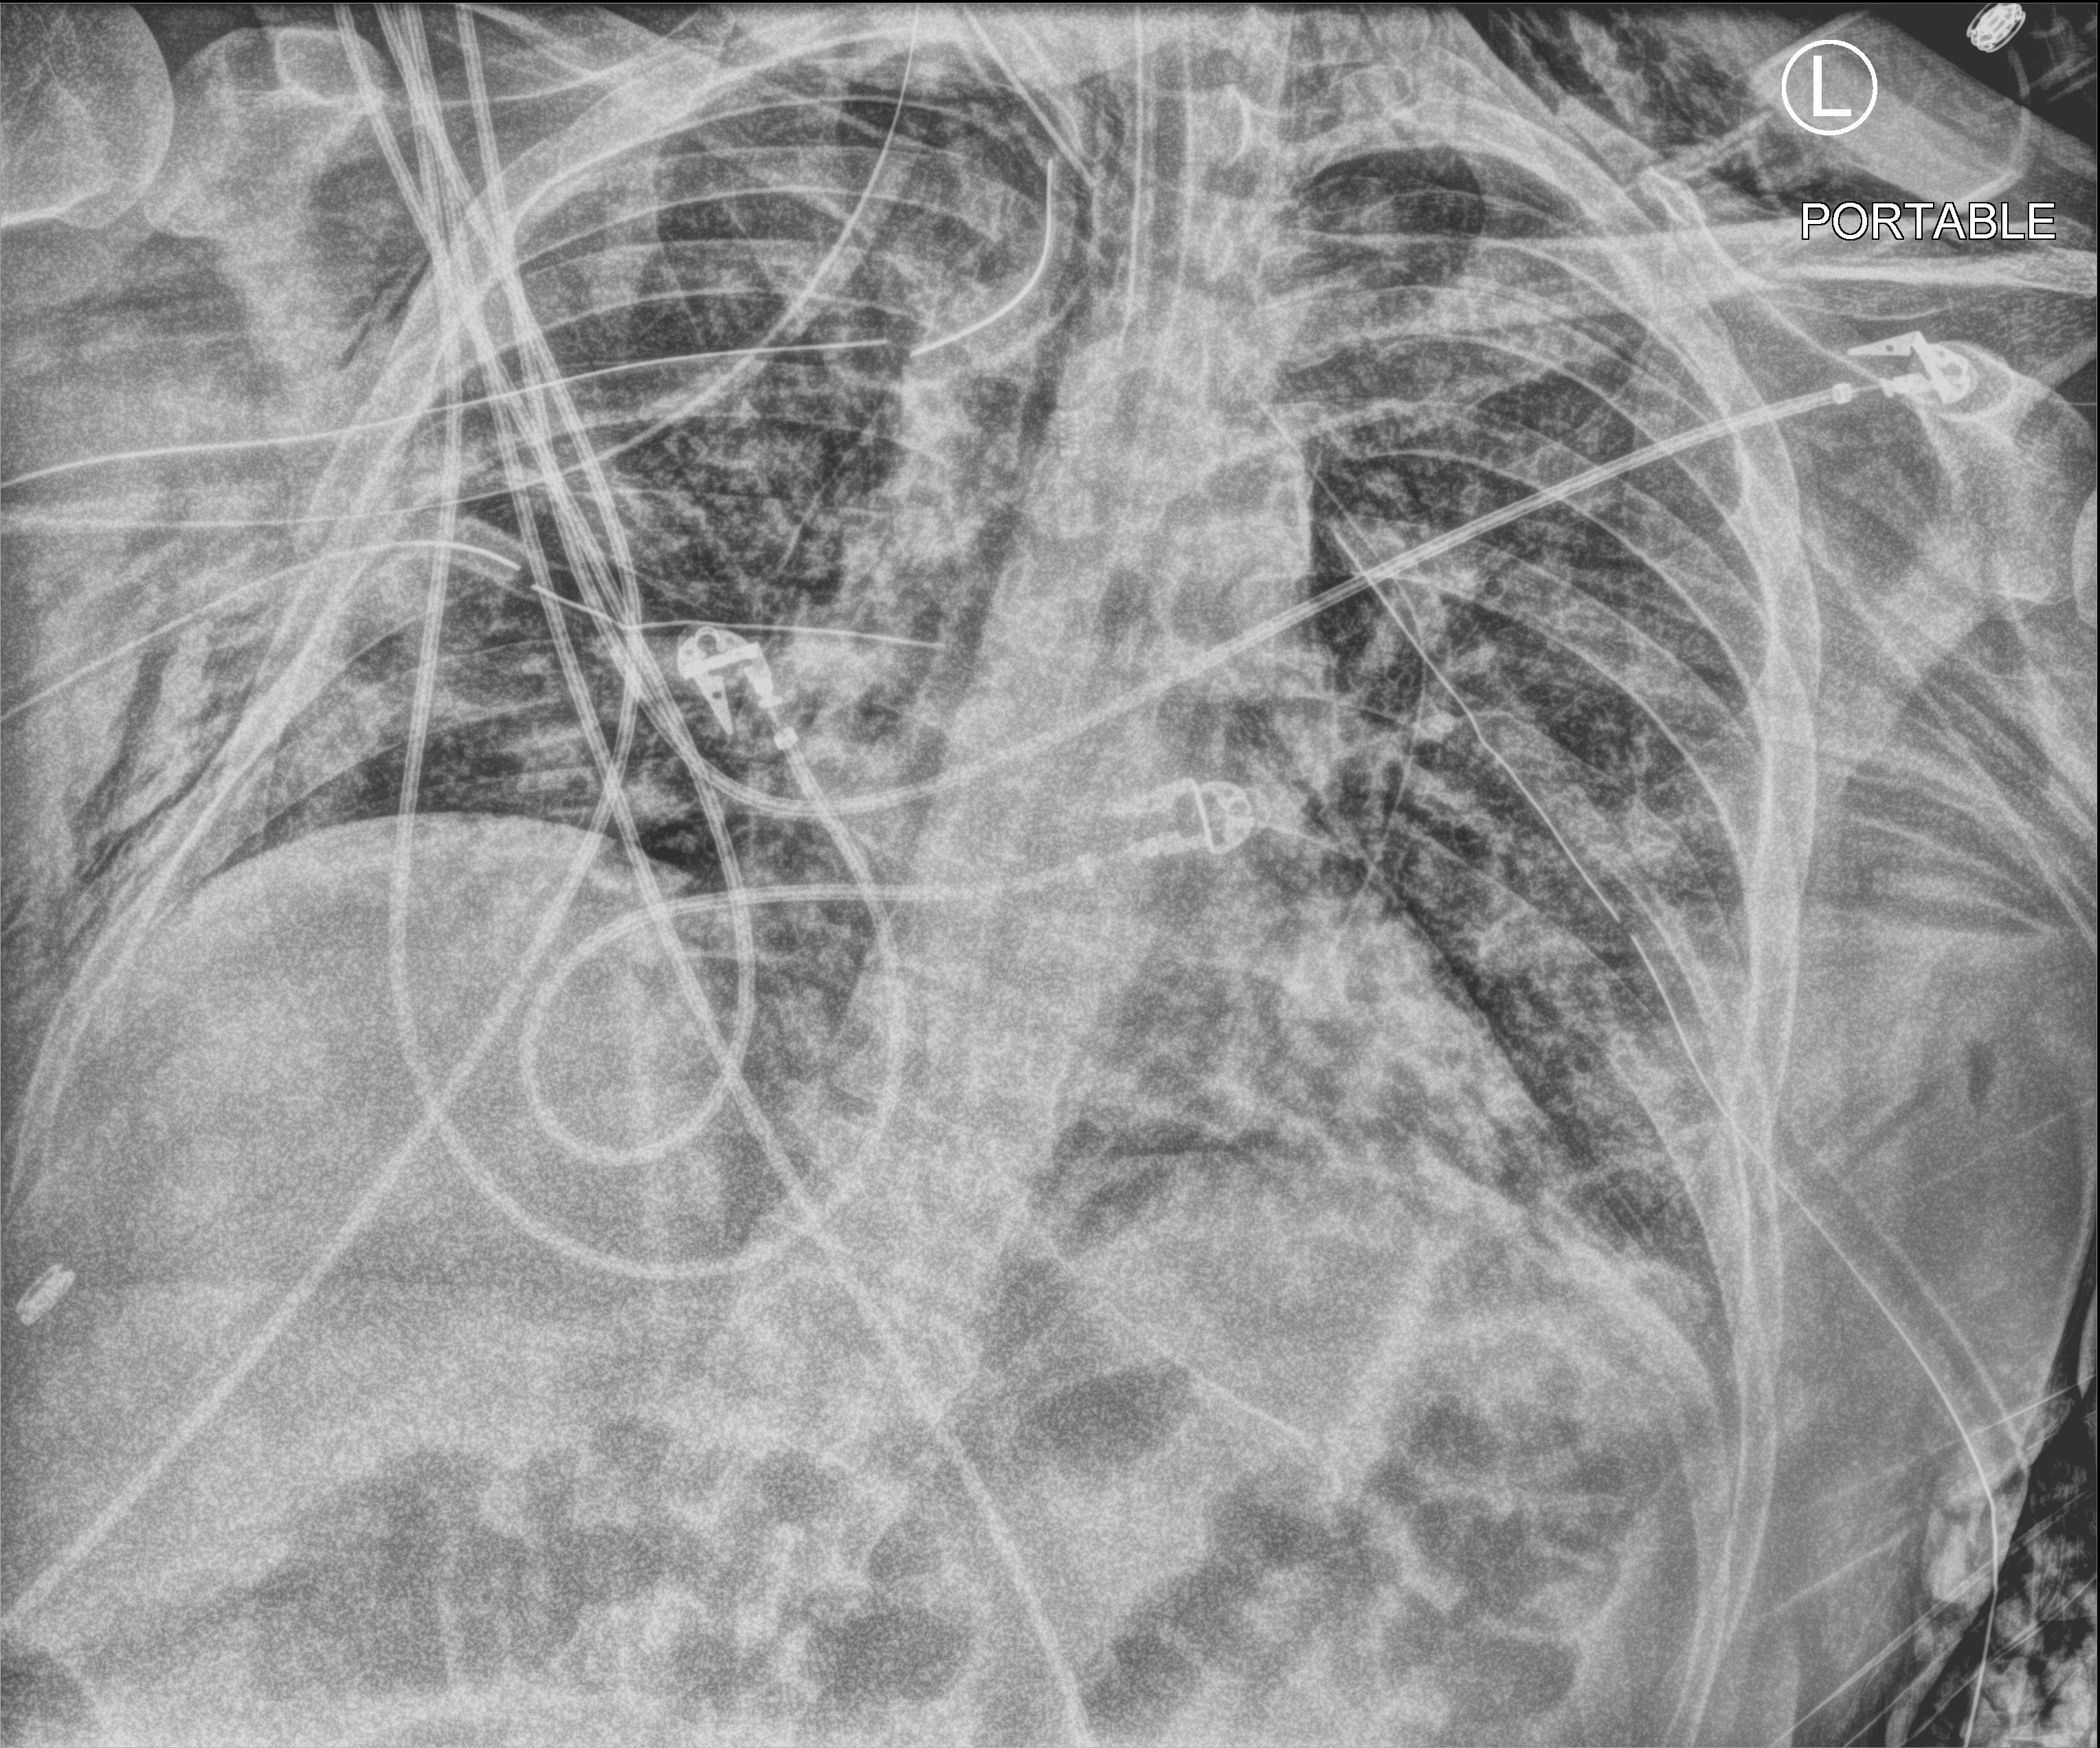
Chest X-ray (portable), anteroposterior (AP) projection. Patient hospitalised with COVID-19; male, aged 18–59 years.
Admission-level facts for this patient (not findings on this image; timing relative to this image not recorded):
- mechanically ventilated during this hospital stay: yes
- length of hospital stay: 63 days